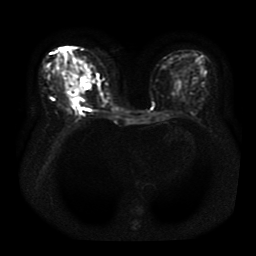
Breast MRI, one axial slice; slice 16 of 41 in the series (ordered by position); diffusion-weighted series; image 2 of 4 stored at this slice position (different b-values; order by instance number); 1.5 T; 256 × 256 image matrix, field of view 330 × 330 mm. Female patient.
Structures marked on this image (manually delineated by an expert):
- tumour on diffusion-weighted imaging: bounding box [x1, y1, x2, y2] px = [68, 79, 80, 99]